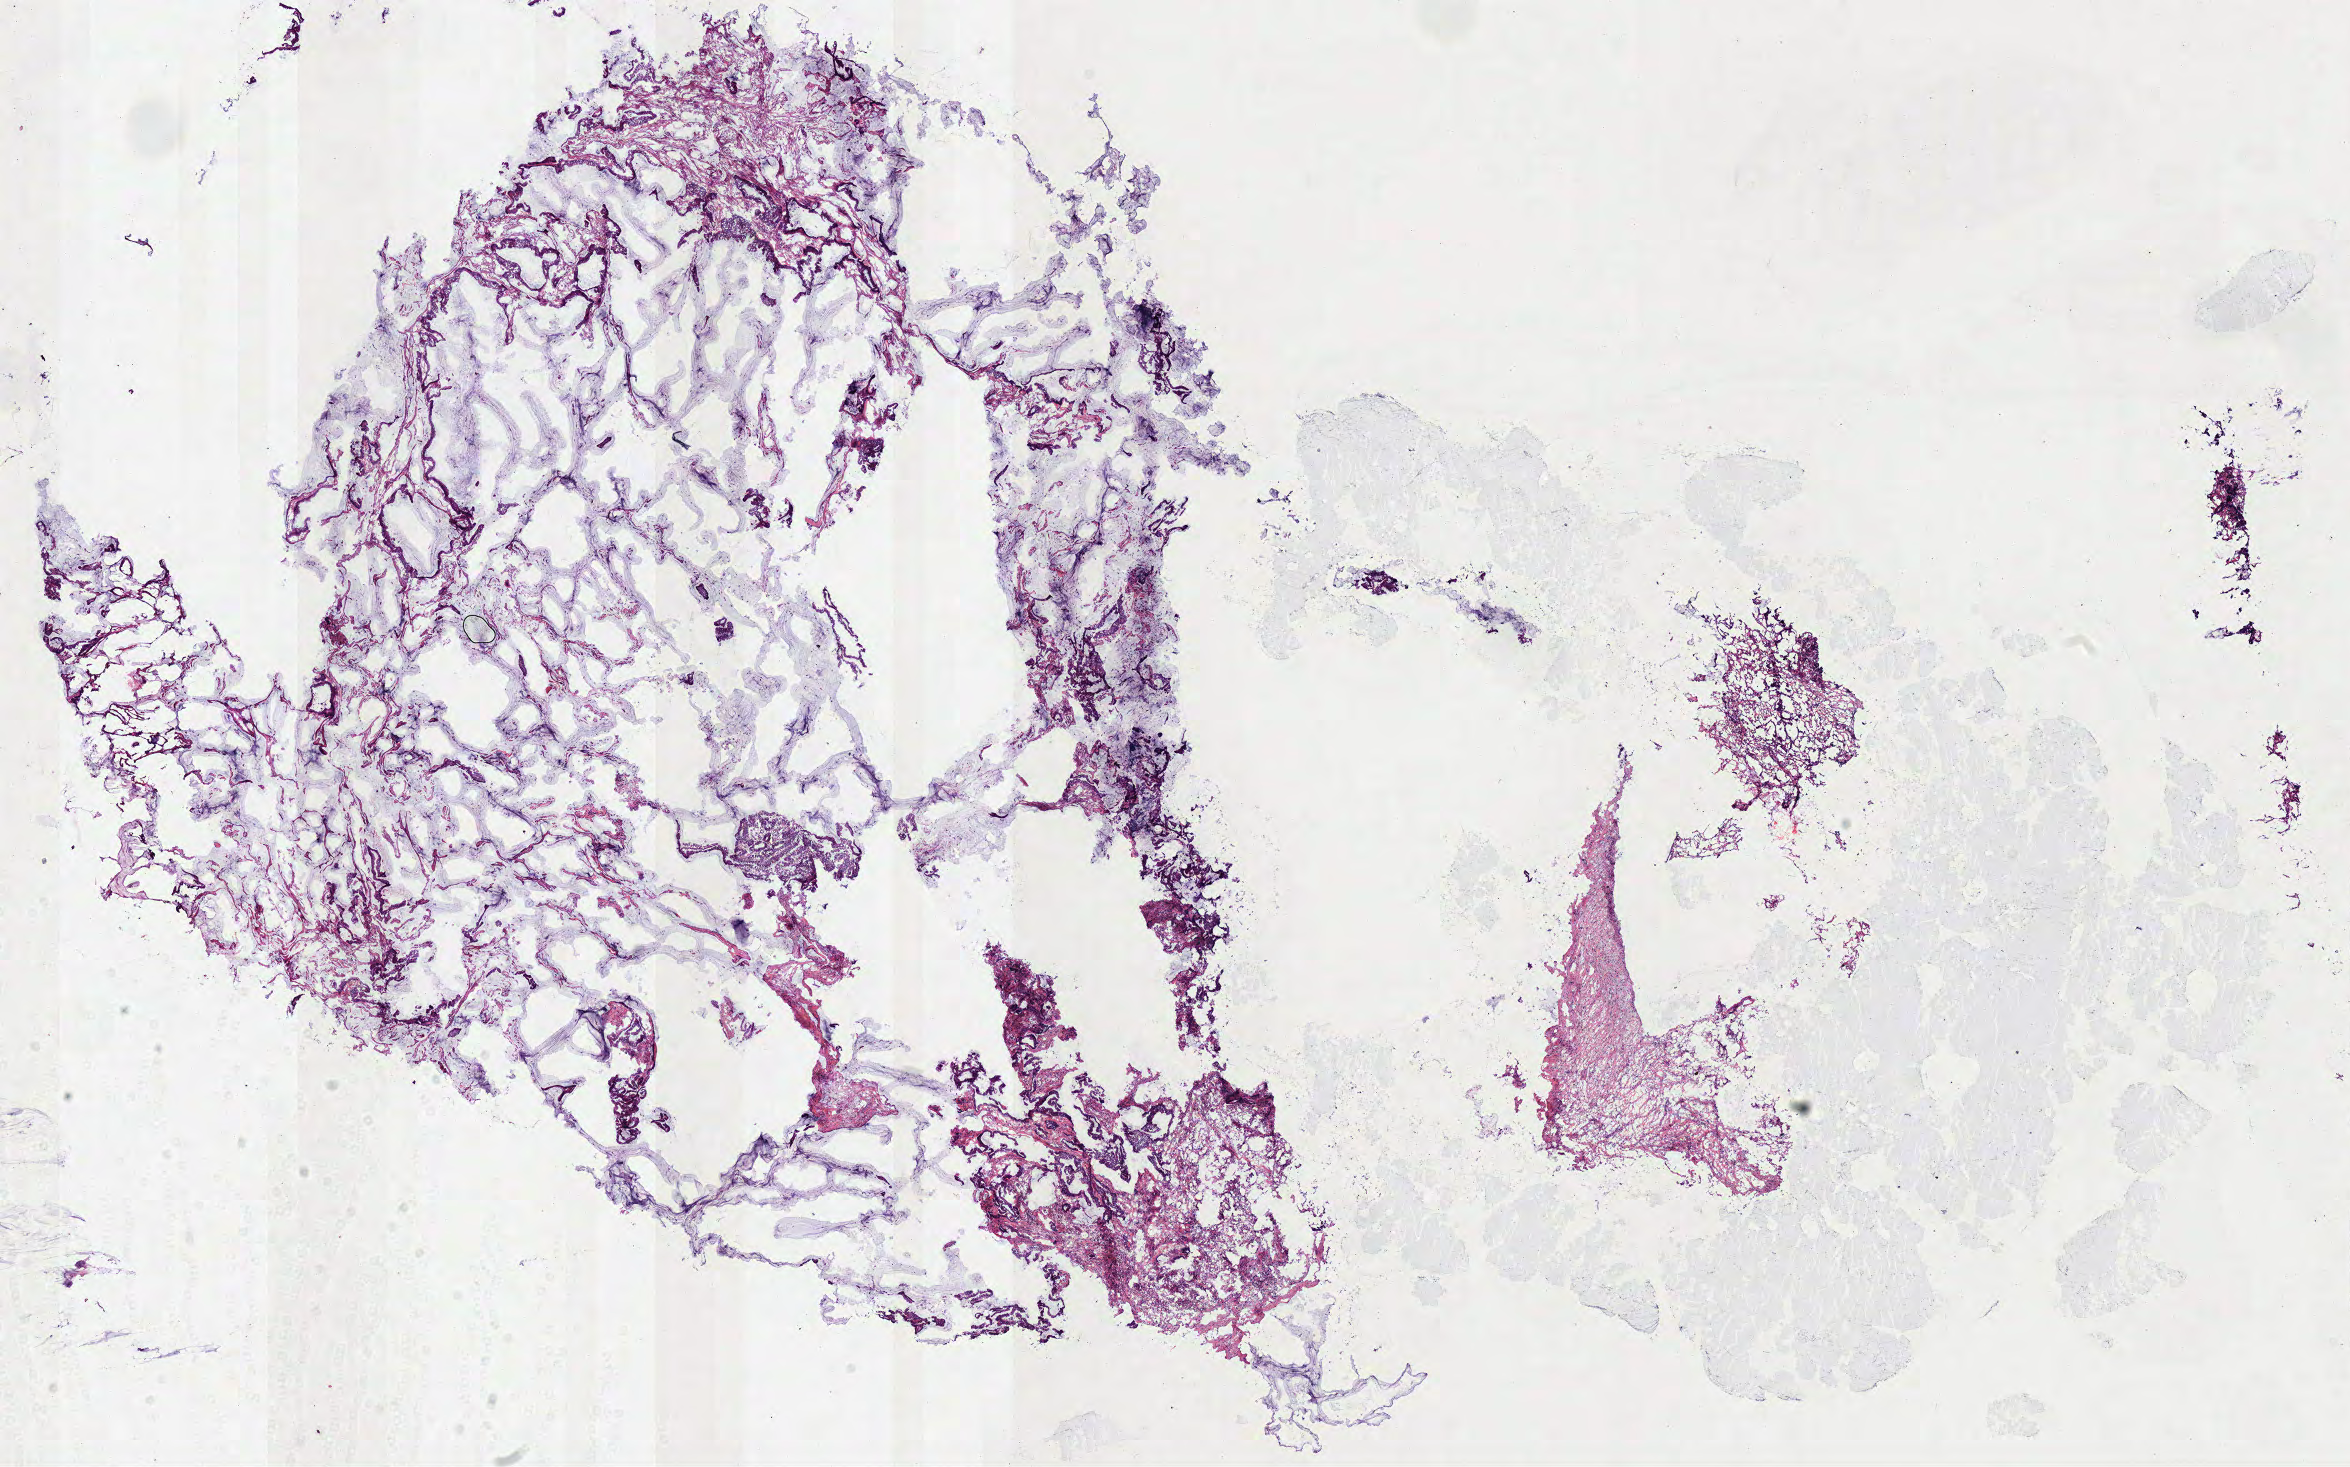
Digitized Hematoxylin and eosin (H&E) stained tissue section (whole slide) — shown as a low-resolution overview of the whole scanned area (about 18.5 x 11.6 mm, slide scanned at 40x). Frozen section. Sample: primary tumour, colon. Patient: female, age at initial diagnosis 70 years. Pathologist review of this section (percent, as recorded): tumour cells 90%, tumour nuclei 85%, normal cells 0%, stromal cells 10%, necrosis 0%.
• pathologic diagnosis: Adenocarcinoma, NOS (sigmoid colon)
• AJCC pathologic stage: IIA (7th edition)
• lymph nodes positive (case pathology): 0 of 12 examined